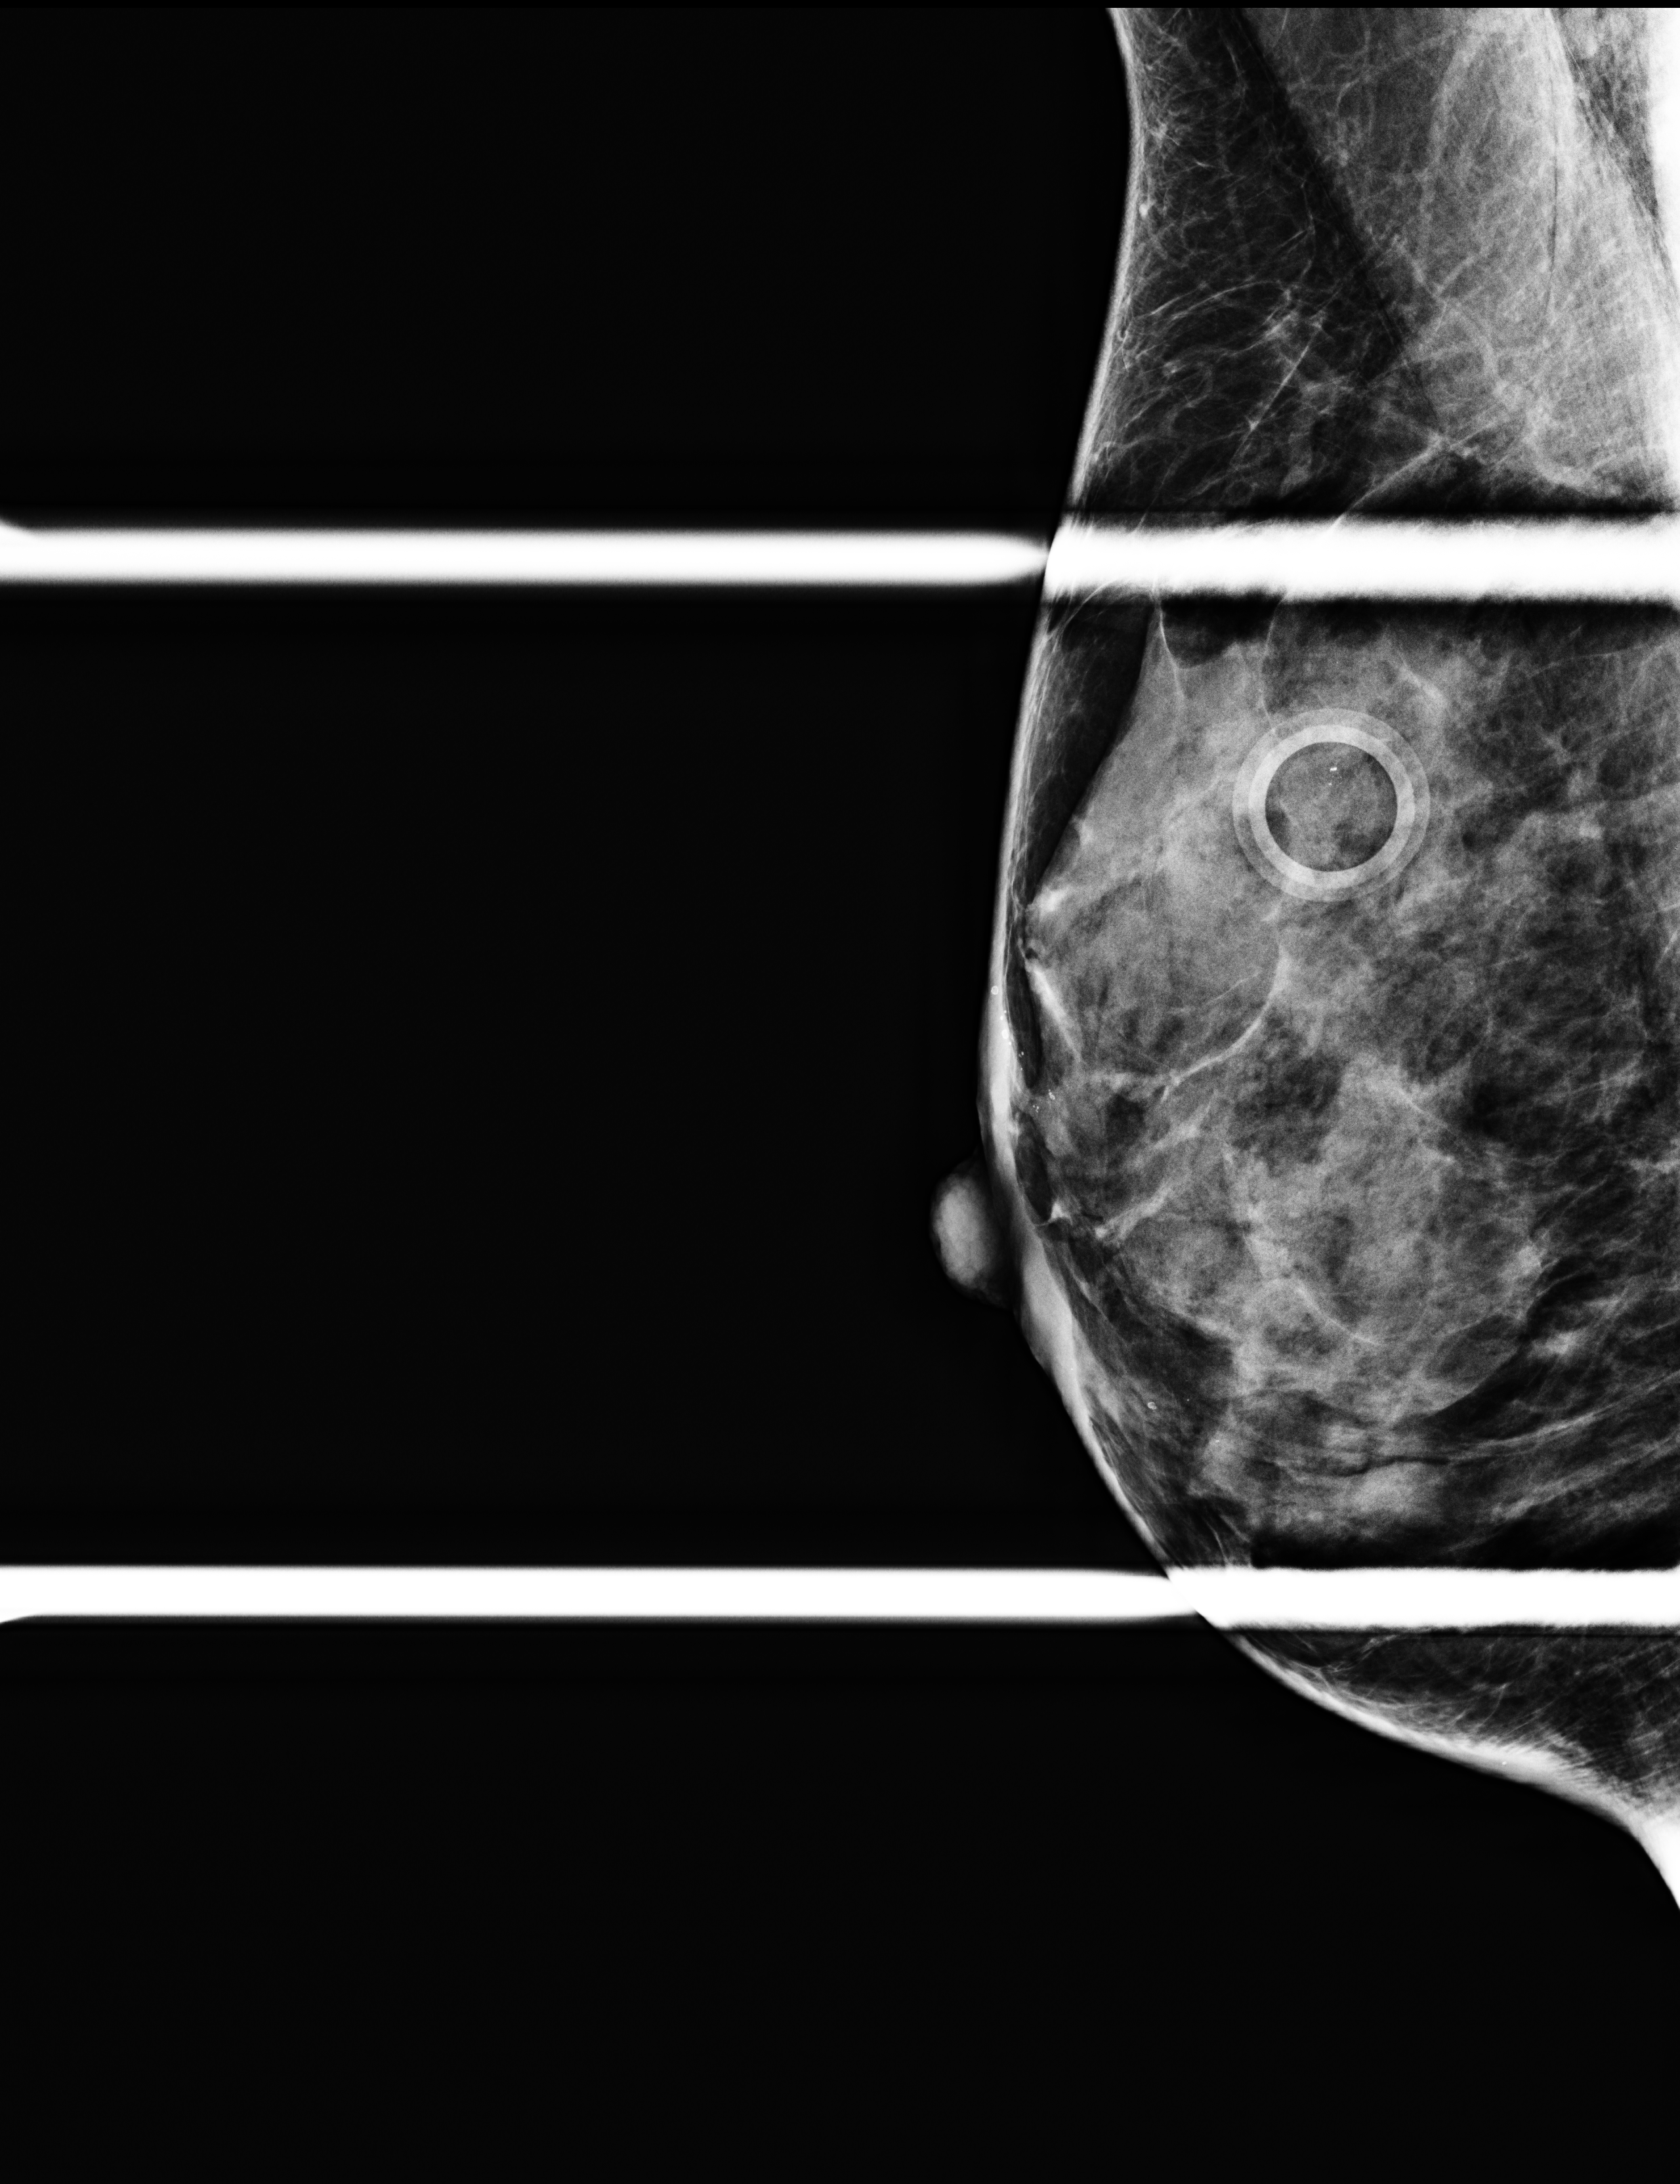
Full-field digital mammogram (FFDM); right breast; MLO view (spot compression); additional (diagnostic) view; system: Selenia Dimensions. Female patient, age 56 years.
Breast density at the screening exam (both breasts): heterogeneously dense (BI-RADS density category c). Final BI-RADS category for the screening round (tomosynthesis exam, both breasts): category 2. Recall: recalled for additional imaging after this screen.